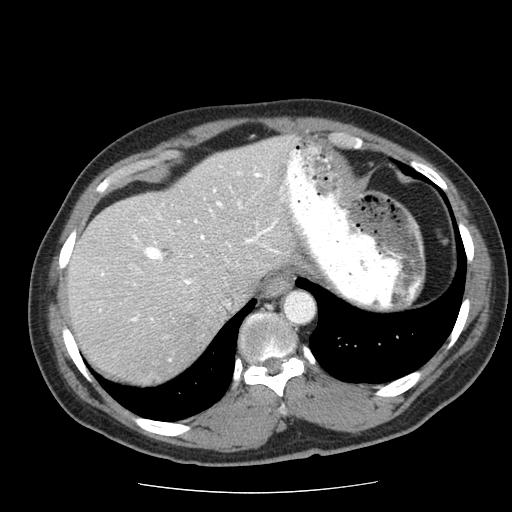
Contrast-enhanced abdominal CT (liver protocol), one axial slice; slice 49 of 85 in the series (ordered by position); 120 kVp; soft-tissue window (W 400 / L 40 HU); 2.5 mm slice thickness; 512 × 512 image matrix. From the clinical record (not read from this slice): diagnosis: hepatocellular carcinoma (patient treated with transarterial chemoembolisation; whether this scan precedes or follows treatment is not stated here); TNM stage (as recorded): Stage-IIIA; Child-Pugh class: A; tumour differentiation: well differentiated; tumour size: 8 cm.
Annotated regions visible in this slice (semi-automatic segmentation, software-assisted and operator-edited):
- liver parenchyma outside the tumour (the mass and vessels are separate outlines, so this box may not span the whole liver): bounding box (x1, y1, x2, y2) in pixels: (66, 136, 348, 384)
- liver vessels: (100, 165, 348, 361)